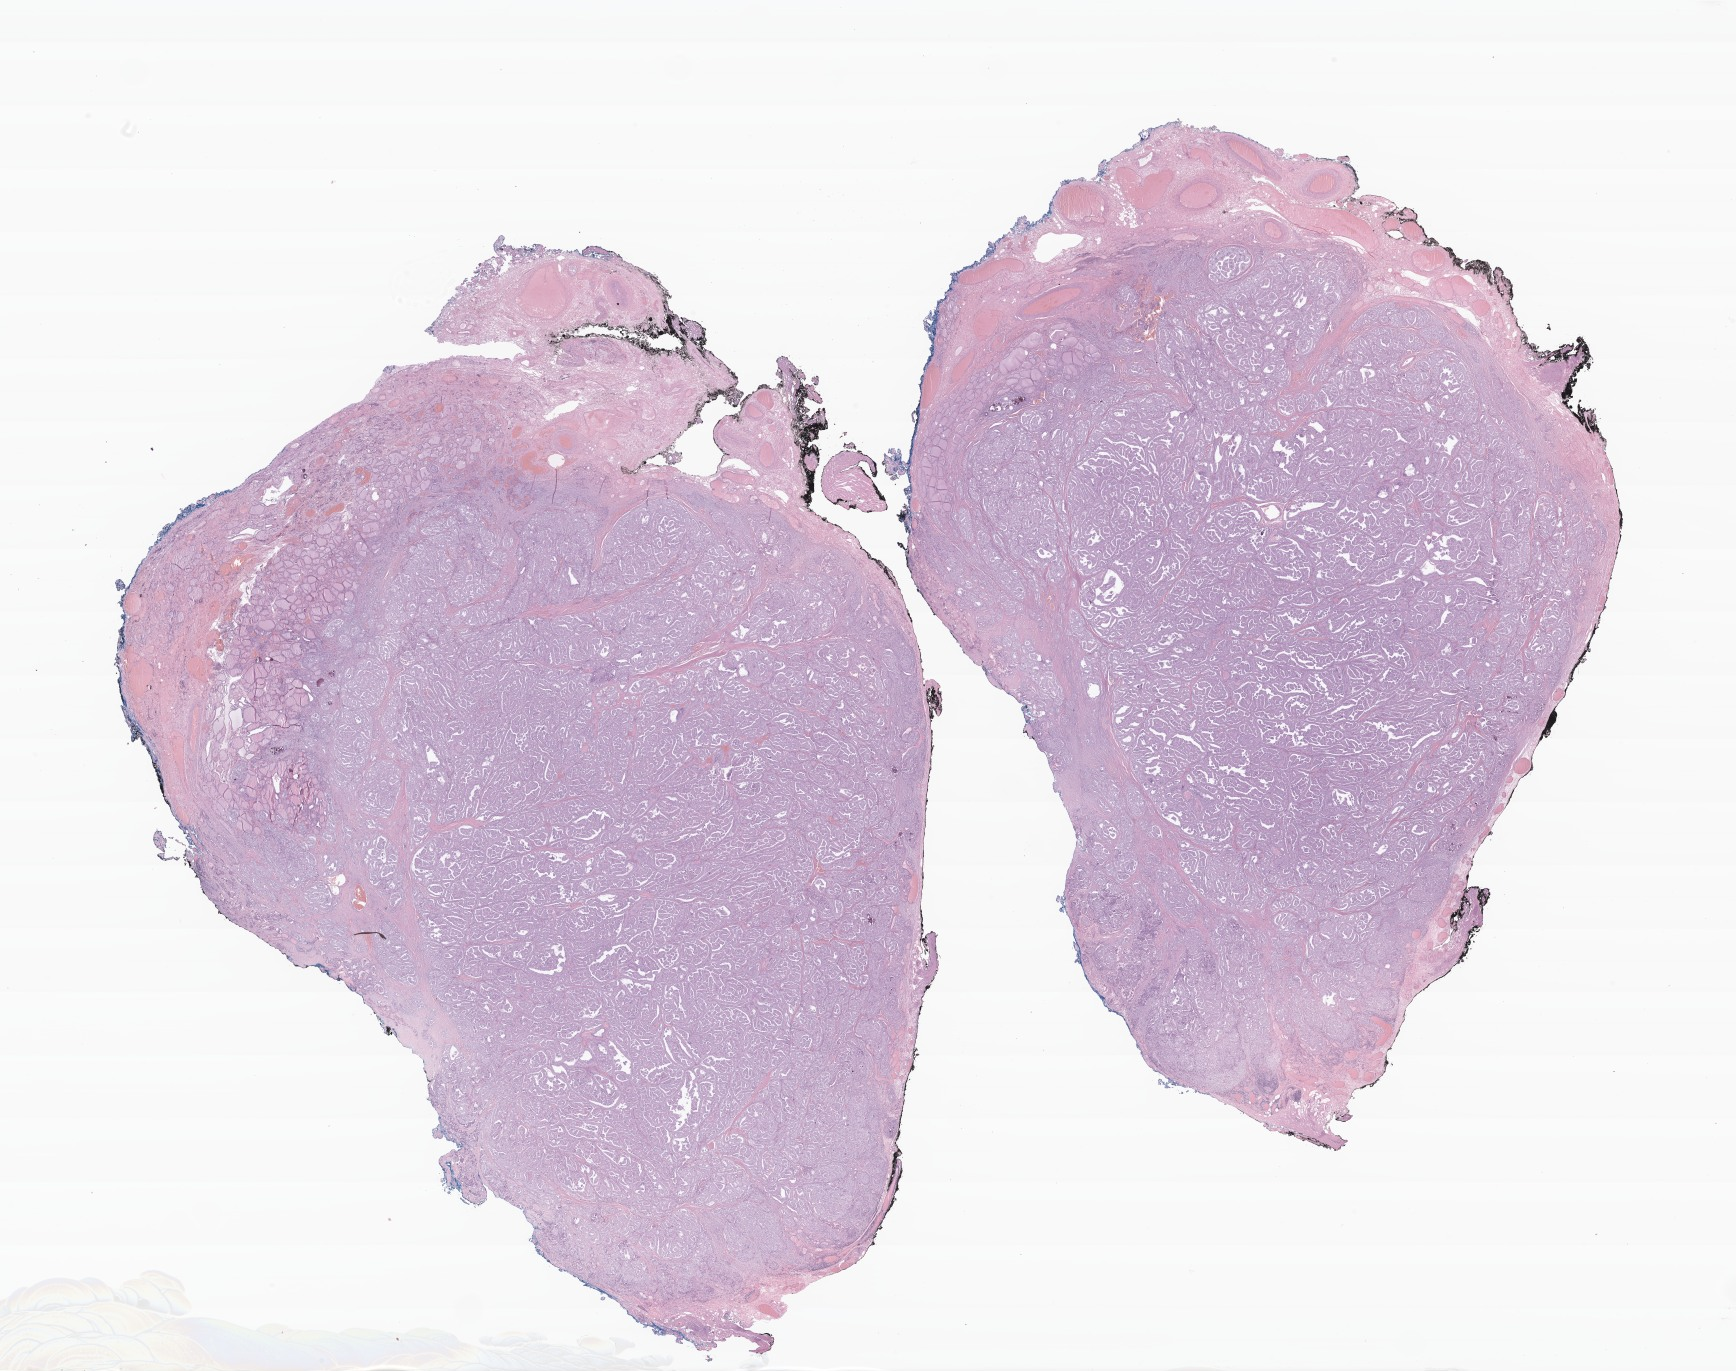
Digitized H&E-stained section of tumor tissue from the thyroid — a low-resolution overview of the entire scanned area, about 29.2 x 23.1 mm. FFPE section. Patient female; age 138 months (11 years 6 months).
Diagnosis (ICD-O-3 morphology term): Papillary carcinoma, NOS.